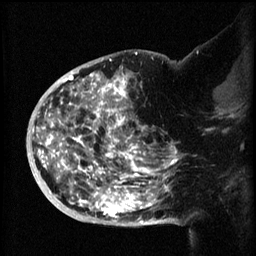
Breast MRI (dynamic contrast-enhanced), one sagittal slice; slice 36 of 60 in the series (ordered by position); 3 images stored at this slice position (order not interpretable as contrast timing); 1.5 T; TE 4.2 ms, TR 8.2 ms; 2 mm slice thickness; 256 × 256 image matrix, field of view 200 × 200 mm. Patient: female, 50 years.
Outlined on this slice (semi-automatically segmented with operator editing):
- analysis volume of interest (the breast-tissue region the enhancement analysis was run in; not a lesion): bounding box (x1, y1, x2, y2) in pixels: (44, 72, 173, 219)
- tumour enhancement mask (voxels above the 70 % enhancement threshold inside the analysis volume of interest): (44, 72, 173, 219)